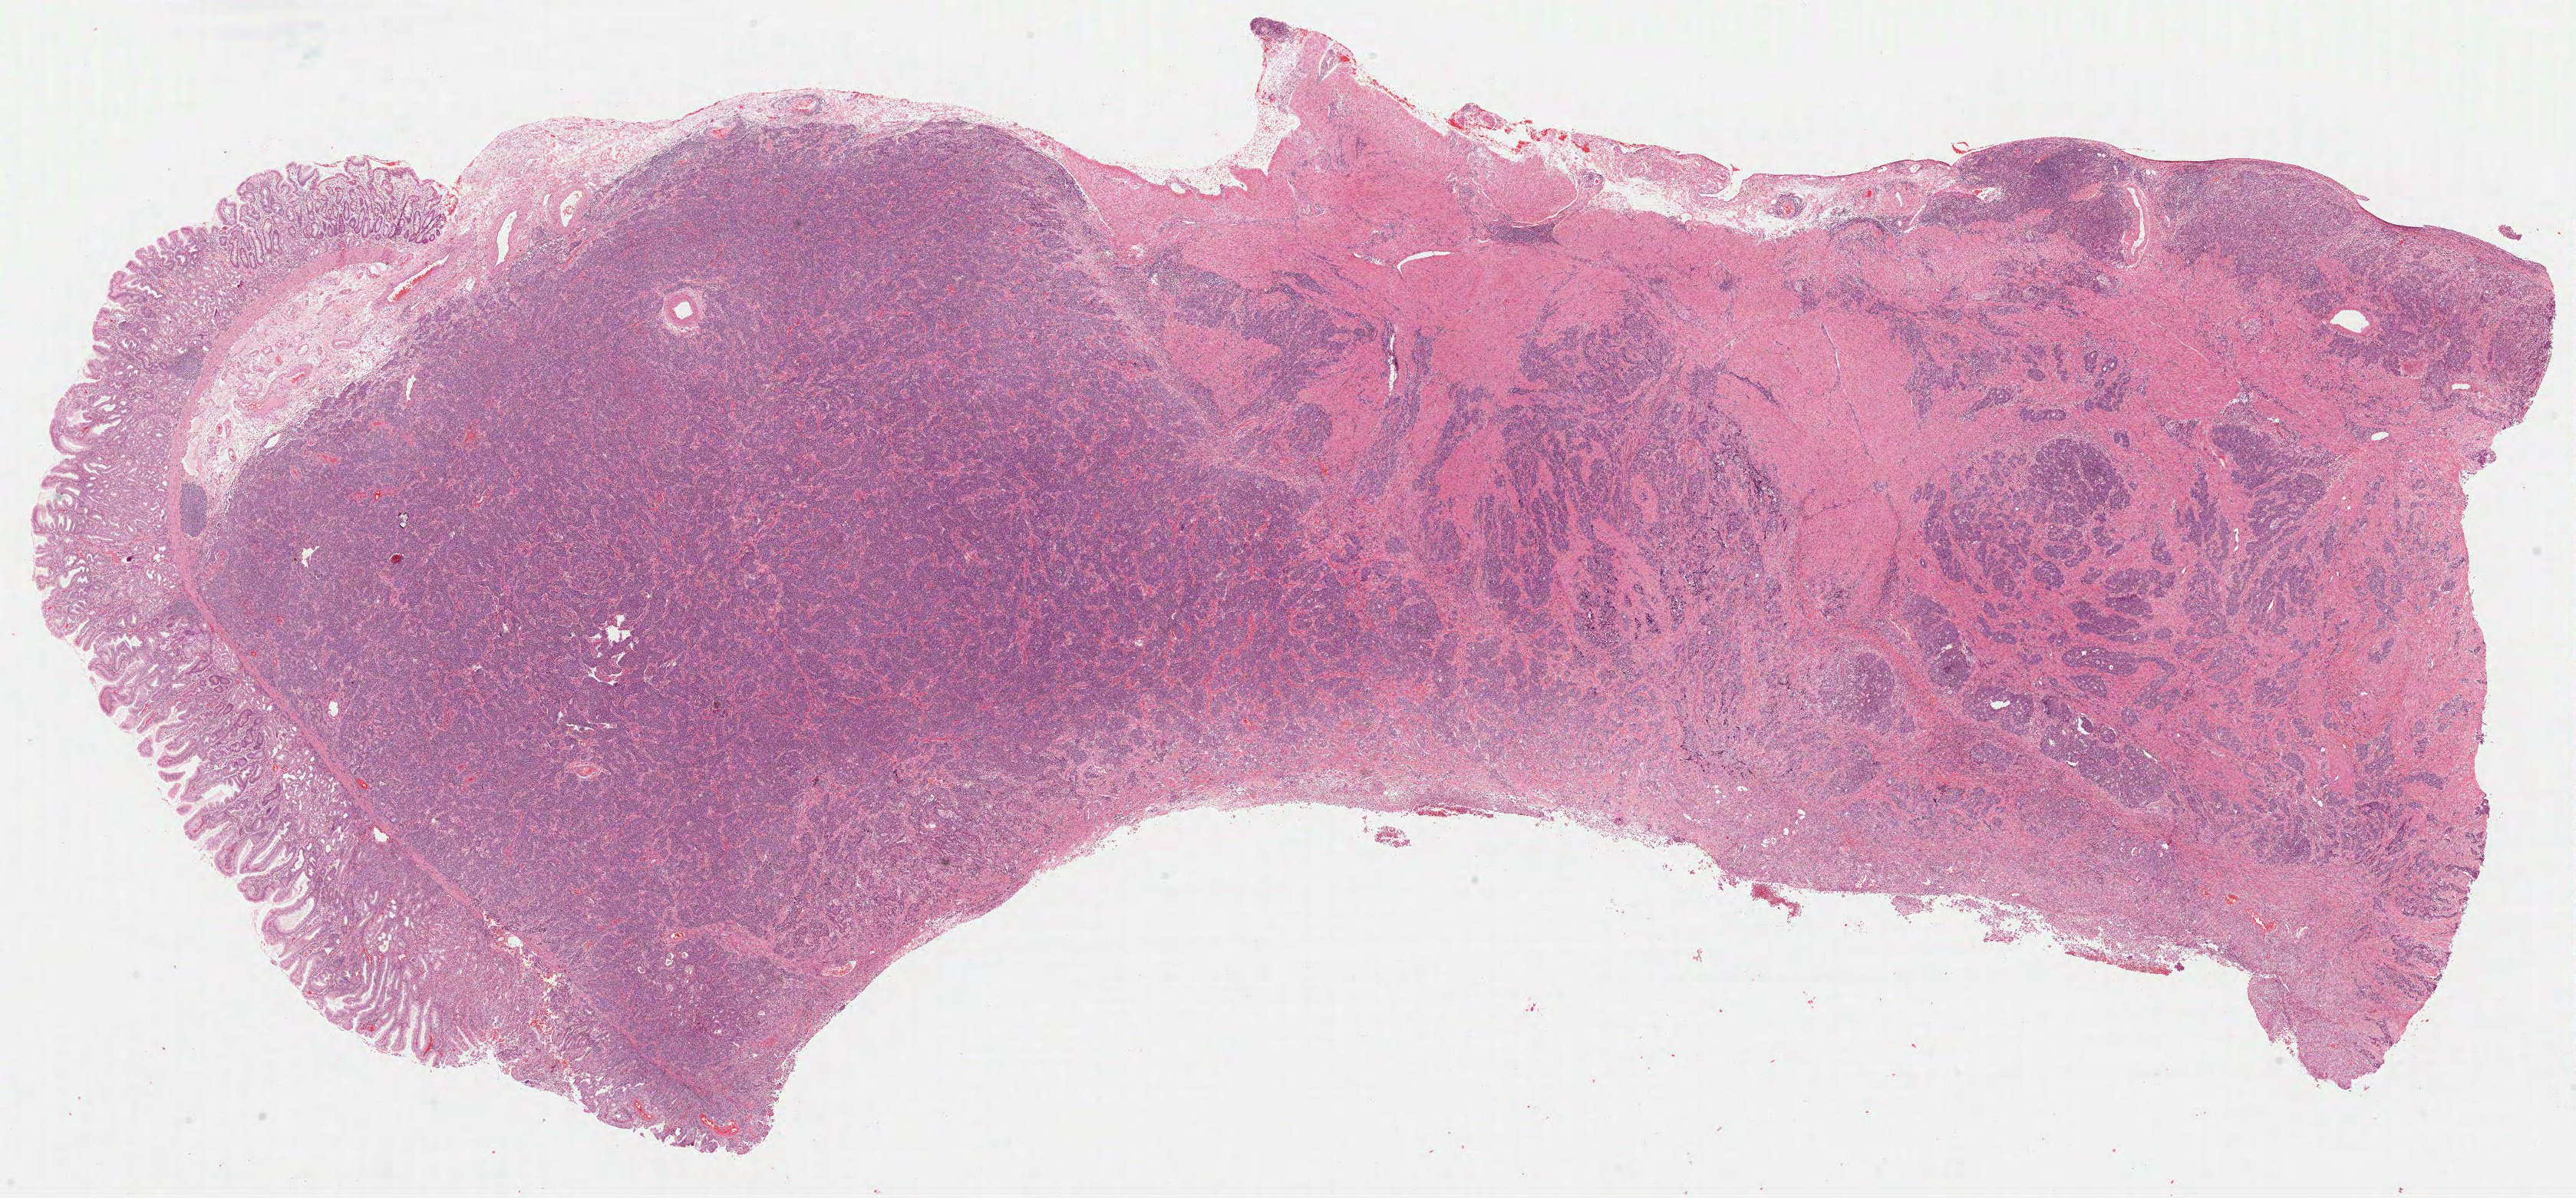
Hematoxylin and eosin (H&E) stained whole-slide image, whole scanned area (about 27.1 x 12.6 mm, slide scanned at 40x) shown as a low-resolution overview; FFPE section; stomach, primary tumour sample. Male, age 59 years at initial diagnosis. Histologic grade: G3 (poorly differentiated).
Histologic diagnosis: Adenocarcinoma, NOS (body of stomach). AJCC pathologic stage: IIB (7th edition). Lymph nodes positive (case pathology): 2 of 19 examined.